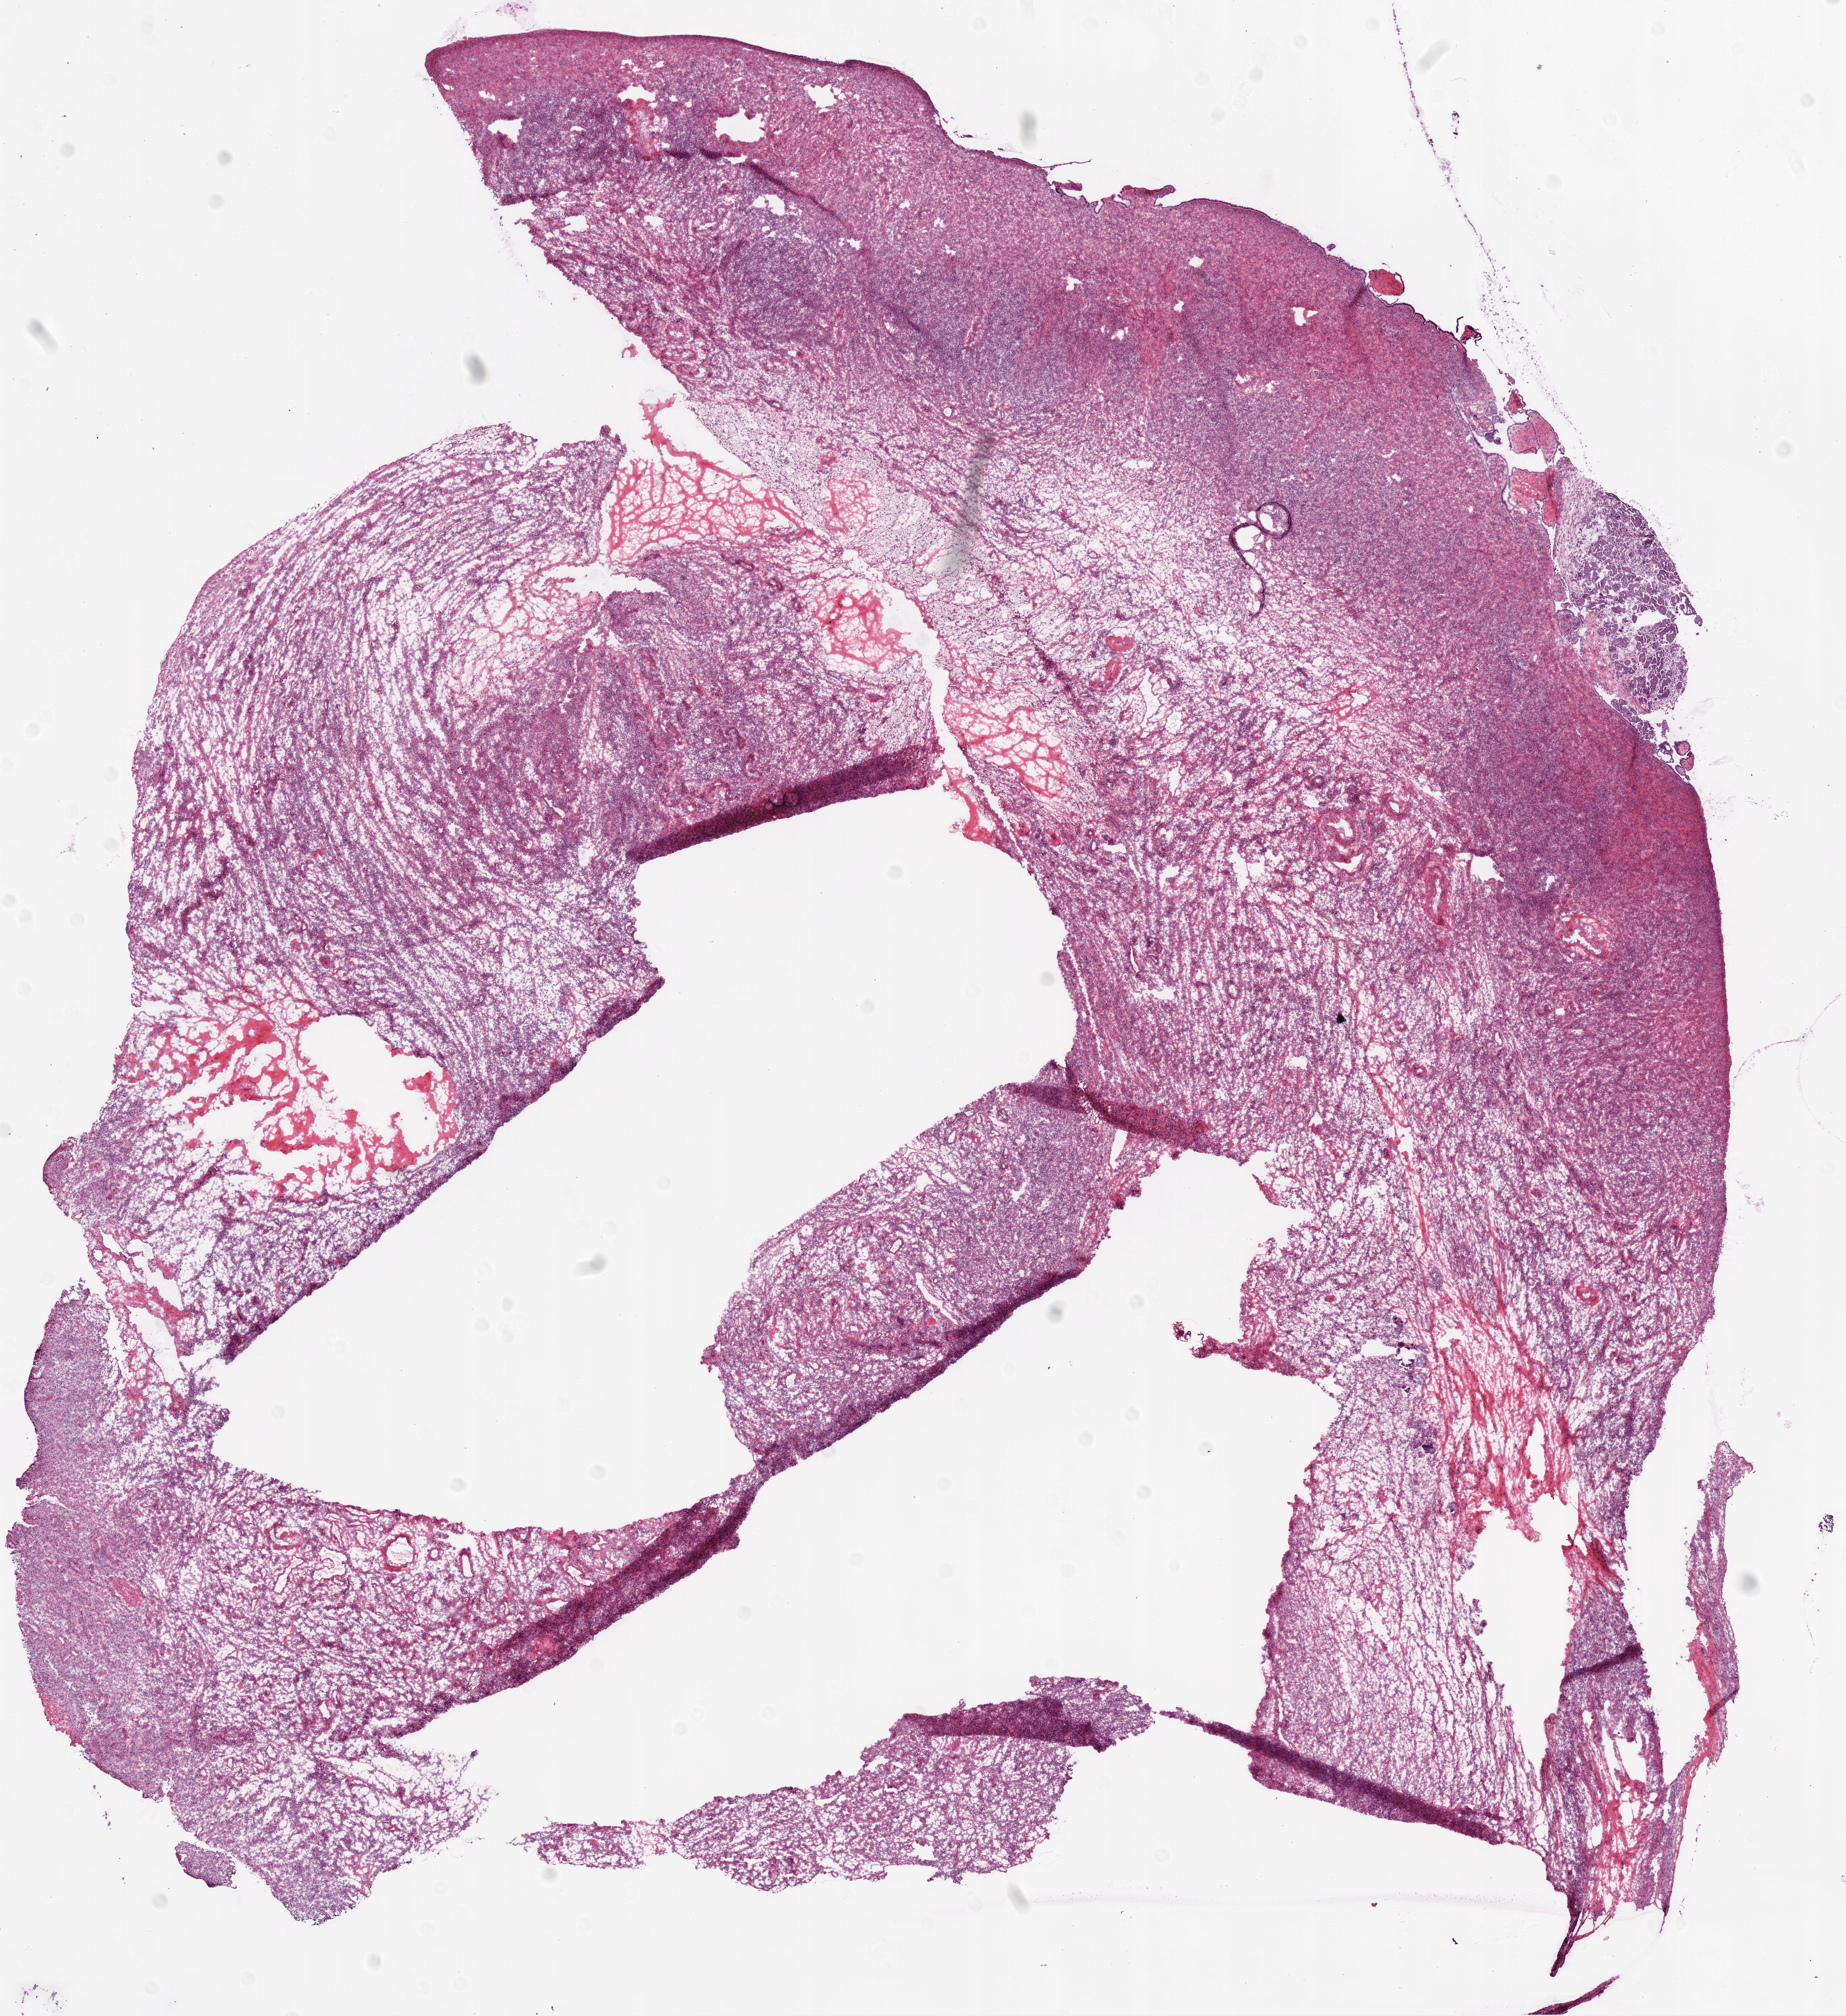
Digitized H&E tissue section (whole slide) — a low-resolution overview of the entire scanned area, about 11.0 x 12.1 mm (from a 20x scan), frozen section, ovary, primary tumour sample. Female, age 38 years at initial diagnosis. Histologic grade: G1 (well differentiated). Pathologist review of this section (percent, as recorded): tumour cells 85%, tumour nuclei 80%, normal cells 0%, stromal cells 0%, necrosis 15%.
- FIGO stage: IV
- pathologic diagnosis: Serous cystadenocarcinoma, NOS
- laterality: bilateral